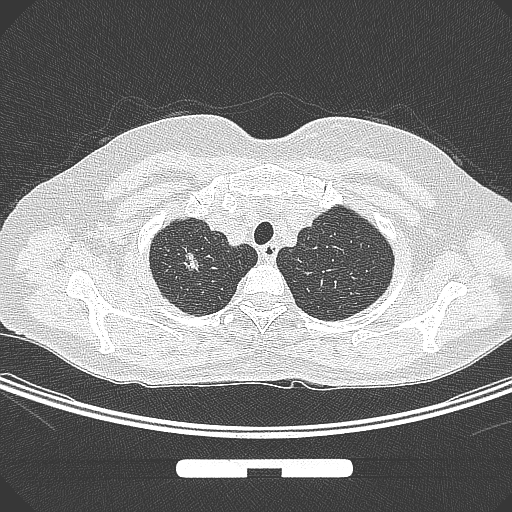
Chest CT, one axial slice. Slice 257 of 295 in the series (ordered by position). 120 kVp. Lung window (W 1500 / L -600 HU). 512 × 512 image matrix, field of view 369 × 369 mm. Patient: female, 58 years. From the clinical record (not read from this slice): clinical TNM (as recorded): T1b N0 M0; histopathological grade: G2-3.
Outlined on this slice (bounding box drawn by a radiologist):
- lung tumour (recorded histology: adenocarcinoma): bounding box (x1, y1, x2, y2) in pixels: (175, 245, 203, 282)